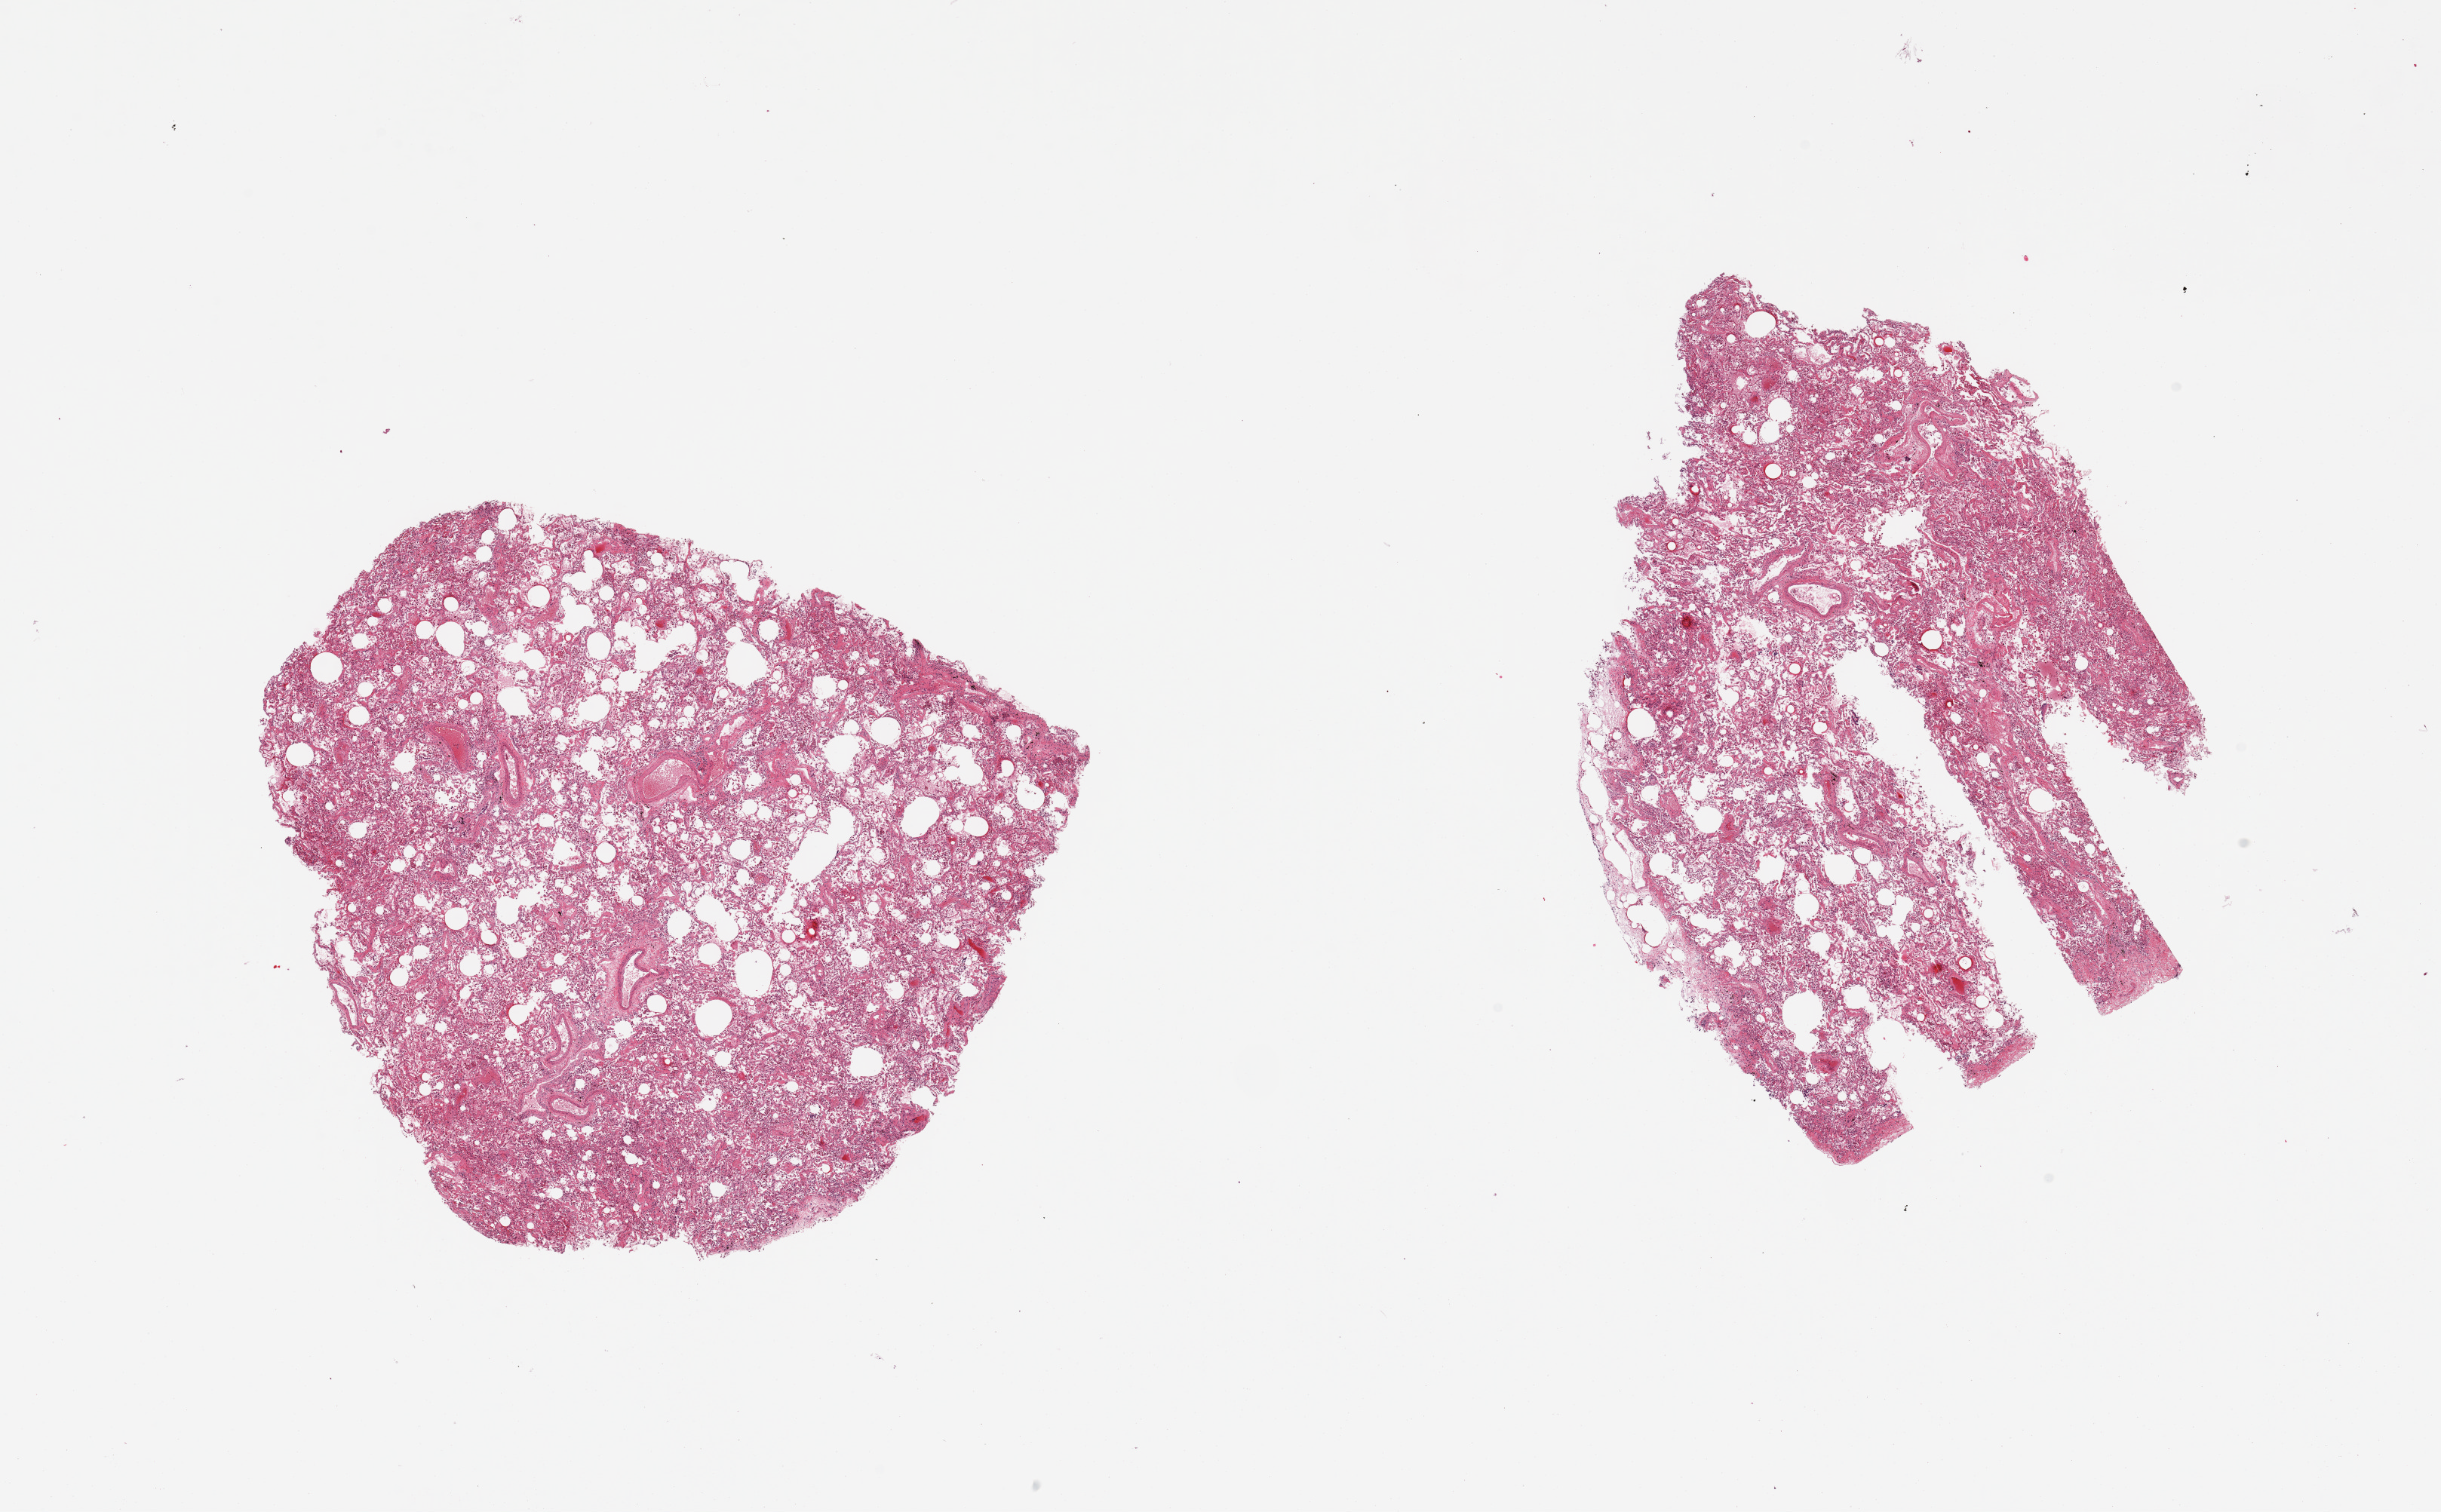
Hematoxylin and eosin (H&E) whole-slide image — whole scanned area (about 25.6 x 15.9 mm, slide scanned at 20x) shown as a low-resolution overview; PAXgene-fixed paraffin-embedded (PFPE) section; target tissue: lung; tissue donor sample. Female donor.
• reviewer comment on this tissue sample: 2 pieces; lung with hemosiderin-laden macrophages in airspaces and some interstitial fibrosis